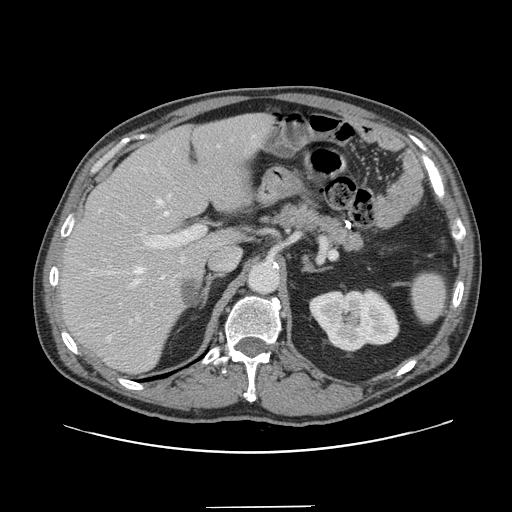
Contrast-enhanced abdominal CT, one axial slice; intravenous contrast given; soft-tissue window (W 400 / L 40 HU); 2.5 mm slice thickness; 512 × 512 image matrix. Male patient, age 64 years. From the clinical record (not read from this slice): diagnosis: colorectal cancer liver metastases, imaged before liver resection; multiple liver metastases: yes; largest metastasis: 3.5 cm; disease in both lobes: yes.
Annotated regions visible in this slice (outlined manually by an expert reader):
- hepatic veins: box from (x=107, y=135) to (x=255, y=323) px
- liver: (x=62, y=115)–(x=271, y=372)
- planned liver remnant (the part of the liver to remain after resection): (x=62, y=115)–(x=269, y=373)
- portal vein (with intrahepatic branches): (x=136, y=225)–(x=206, y=321)
- liver metastasis: (x=183, y=280)–(x=197, y=306)